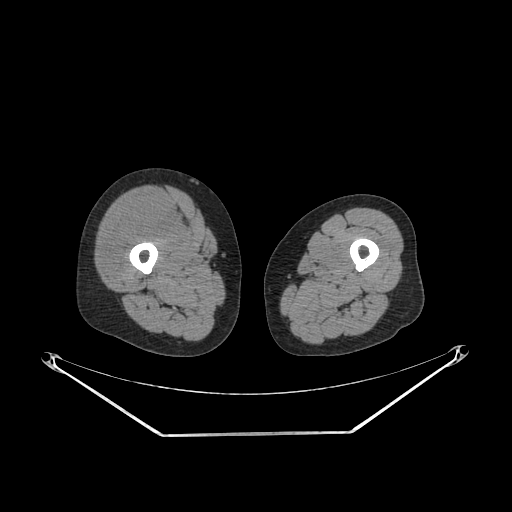
CT of an extremity soft-tissue mass (from a PET/CT study), one axial slice. Soft-tissue window (W 400 / L 40 HU). 512 × 512 image matrix, field of view 500 × 500 mm. Female patient. Case-level facts recorded for this patient, not image findings: histological type: pleiomorphic undifferentiated sarcoma; grade: high; site of the primary tumour: right quadricep.
Structures marked on this image (expert contour drawn on MRI and transferred to this co-registered scan by the dataset authors):
- tumour plus oedema (research contour): bounding box [x1, y1, x2, y2] px = [103, 201, 181, 279]
- tumour (research contour): [114, 203, 179, 229]